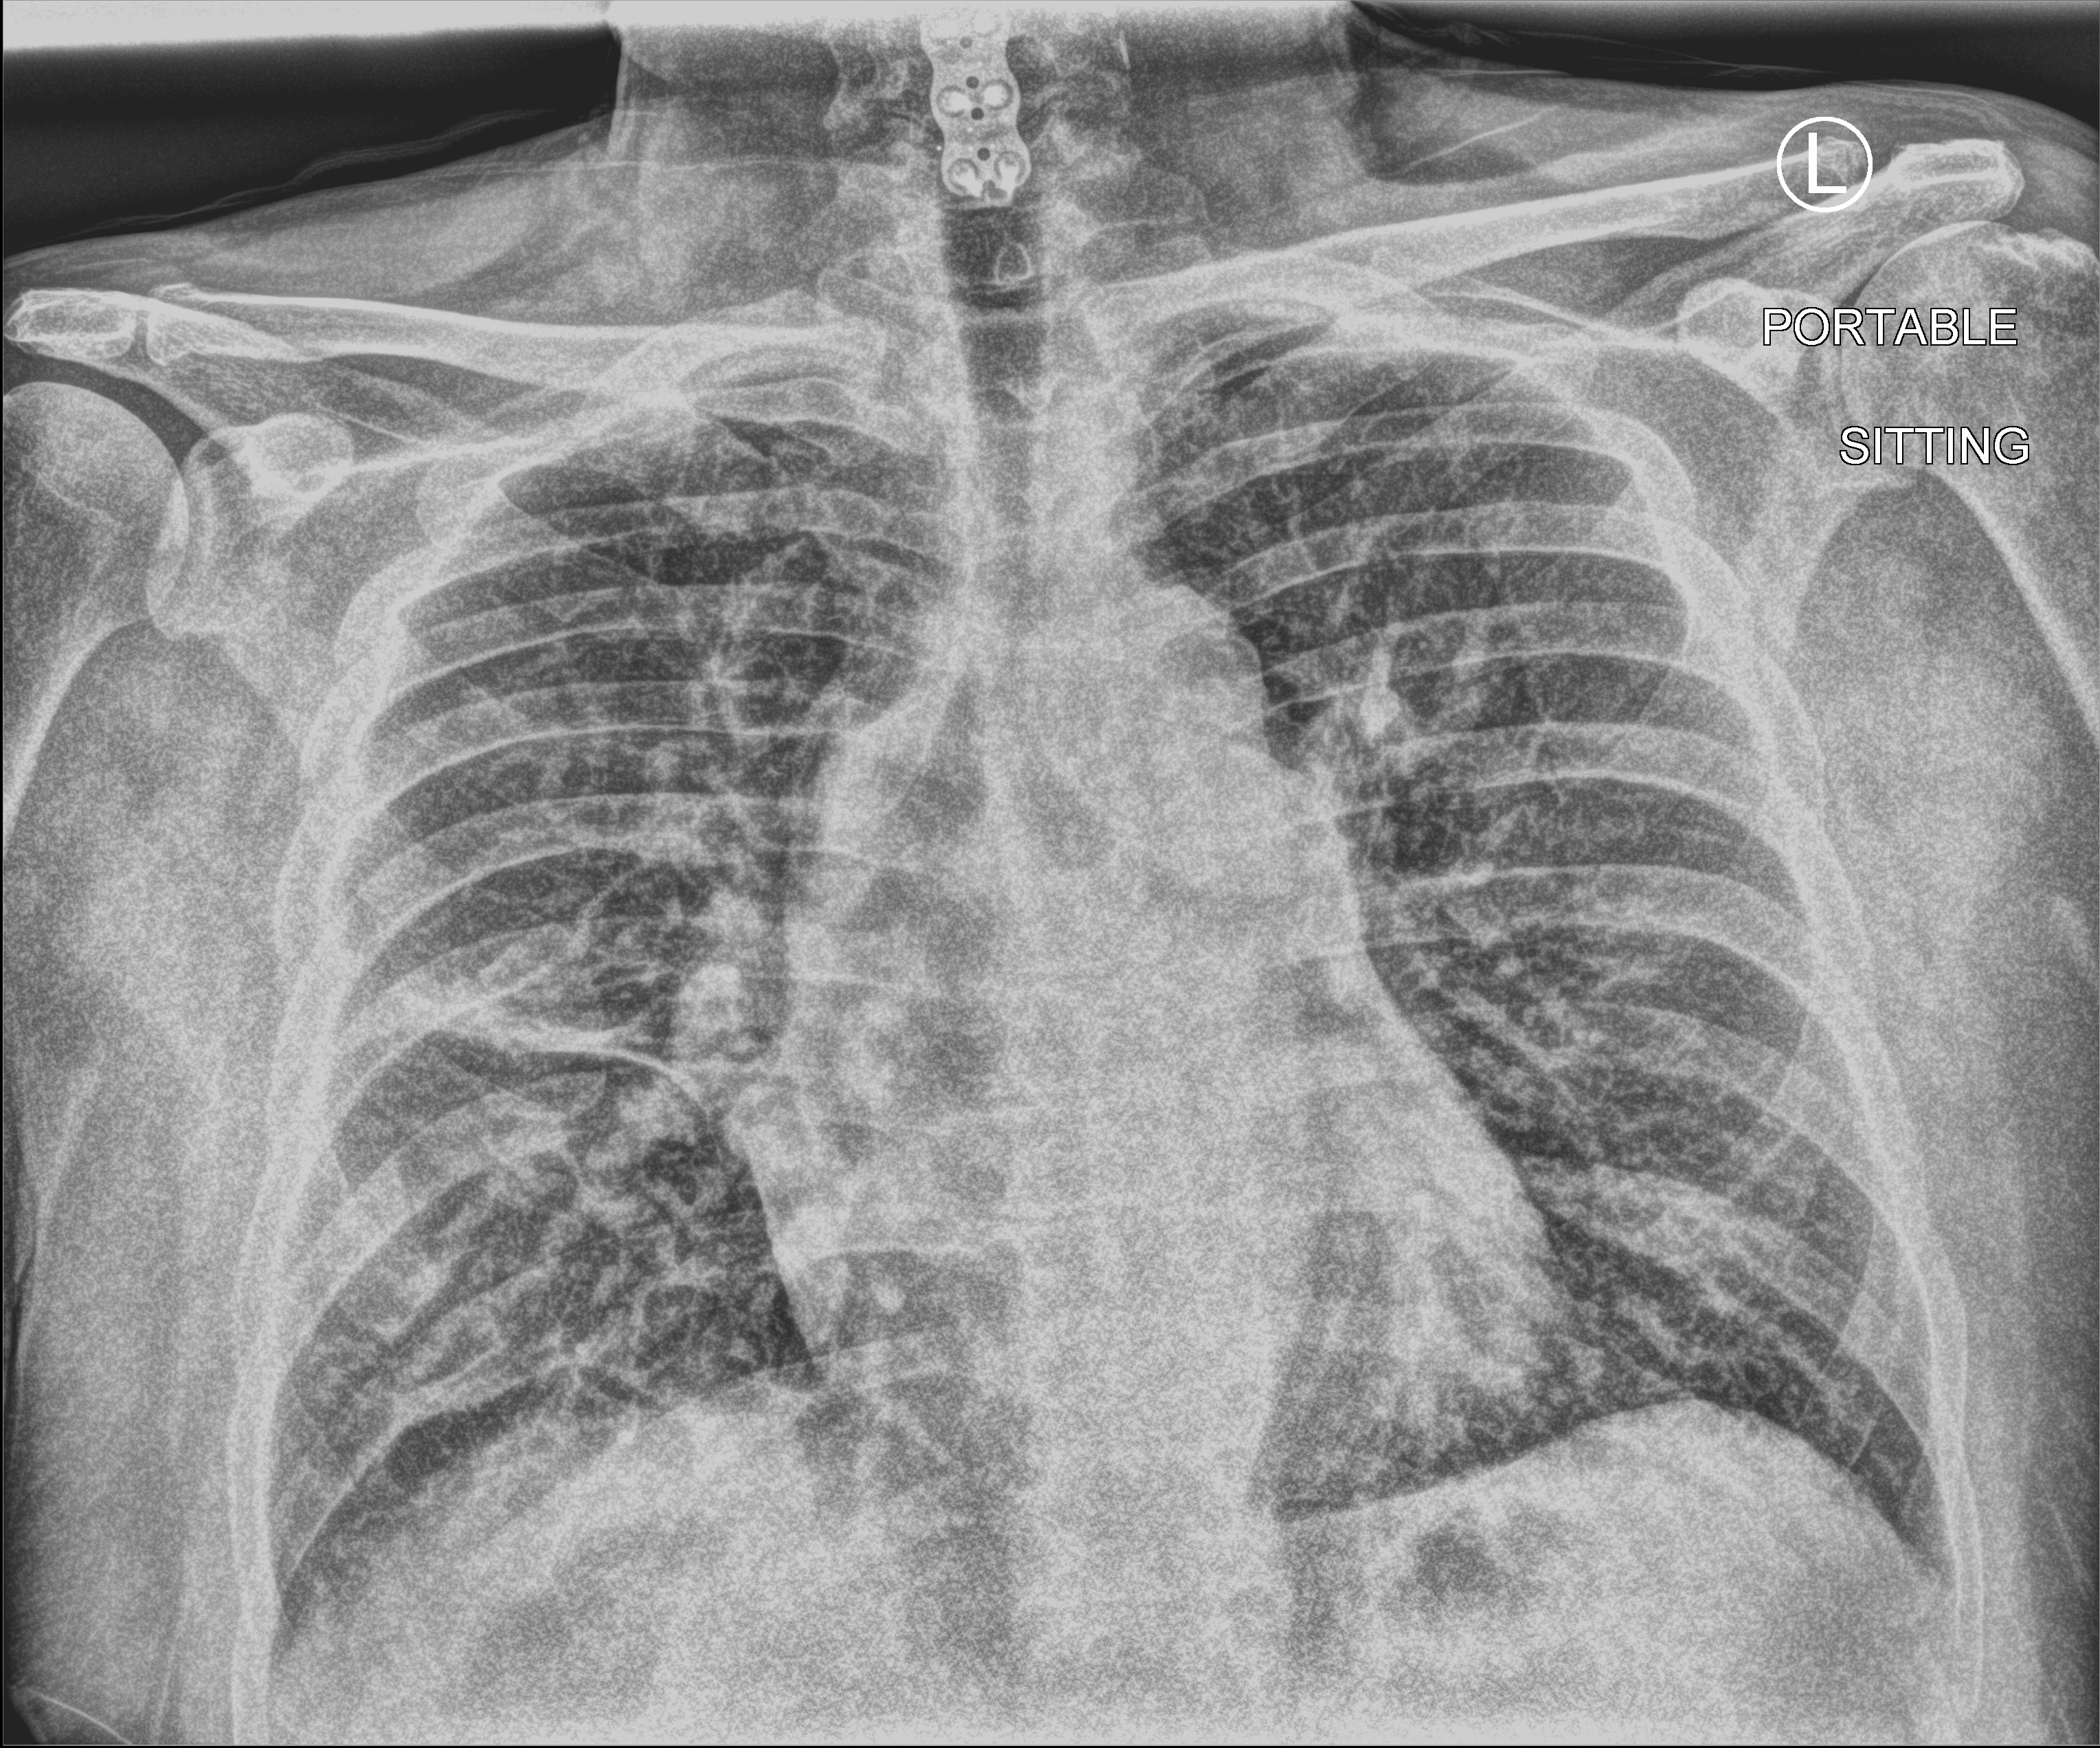
Chest X-ray (portable). Patient hospitalised with COVID-19; male, aged 18–59 years.
Admission-level facts for this patient (not findings on this image; timing relative to this image not recorded):
- admitted to intensive care during this hospital stay: no
- mechanically ventilated during this hospital stay: no